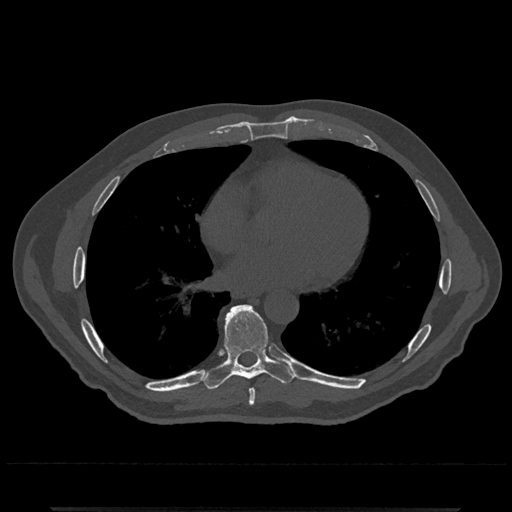
CT including the spine, one axial slice; position 677 of 797 along the scan axis; reconstruction kernel Br40s/3; 120 kVp; bone window (W 1800 / L 400 HU); 0.5 mm slice thickness; 512 × 512 image matrix. Patient: male, 67 years. Case-level facts recorded for this patient, not image findings: primary cancer: prostate.
Annotated regions visible in this slice (semi-automatic segmentation, software-assisted and operator-edited):
- T7 vertebra: bounding box <248,389,256,406> (left, top, right, bottom; pixels)
- T8 vertebra: <202,305,295,390>